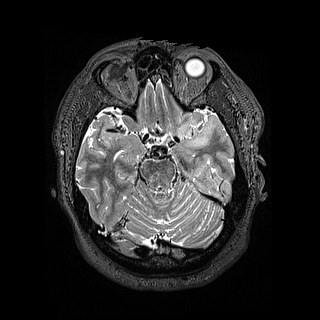
Brain MRI from a brain-tumour surgery series, one axial slice; slice 102 of 144 in the series (ordered by position); 1.2 mm slice thickness; 320 × 320 image matrix, field of view 254 × 254 mm. Case-level facts recorded for this patient, not image findings: histopathology: Astrocytoma; WHO grade: 2; IDH mutation: yes; tumour location: Left Insular.
Outlined on this slice (expert manual segmentation):
- tumour: bounding box <183,114,205,149> (left, top, right, bottom; pixels)